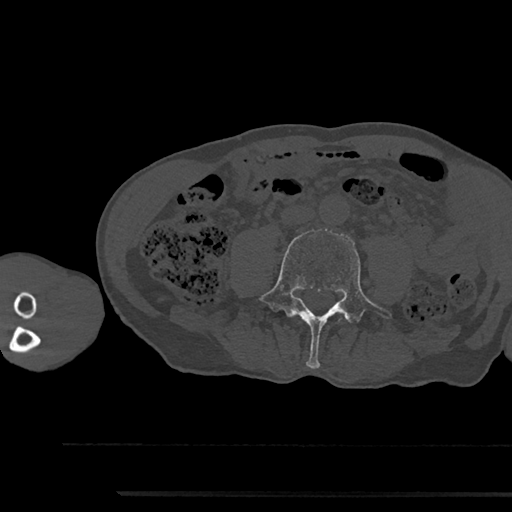
CT including the spine, one axial slice. Slice 421 of 797 in the series (ordered by position). Reconstruction kernel Br40s/3. 120 kVp. Bone window (W 1800 / L 400 HU). 512 × 512 image matrix, field of view 367 × 367 mm. Male patient, age 79 years. From the clinical record (not read from this slice): primary cancer: prostate.
Outlined on this slice (semi-automatic segmentation, software-assisted and operator-edited):
- L4 vertebra: box from (x=257, y=229) to (x=392, y=368) px